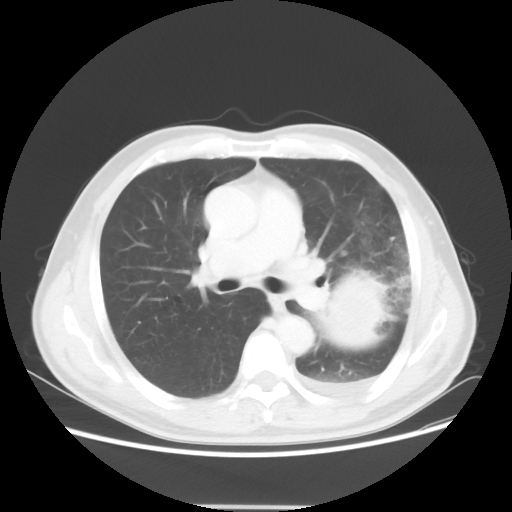
Chest CT, one axial slice; position 32 of 53 along the scan axis; reconstruction kernel STANDARD; lung window (W 1500 / L -600 HU); 5 mm slice thickness; 512 × 512 image matrix, field of view 391 × 391 mm. Patient: male, 60 years. From the clinical record (not read from this slice): clinical TNM (as recorded): T4 N1 M1a; histopathological grade: G3.
Outlined on this slice (rectangle marked by the reading radiologist):
- lung tumour (recorded histology: large cell carcinoma): bounding box <312,259,394,348> (left, top, right, bottom; pixels)